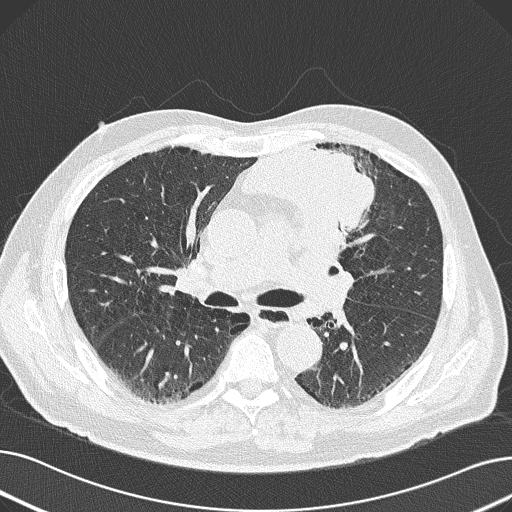
Axial slice from a low-dose chest CT screening exam. Baseline screening round. Lung window (W 1500 / L -600 HU). Lung (sharp) reconstruction kernel (B50f). 512 × 512 image matrix, field of view 370 × 370 mm. Male participant, aged 69 years at enrolment. Former smoker at enrolment.
Lesion marked by an expert reader, box from (x=236, y=132) to (x=385, y=249) px. Screening reader's record for this exam (one nodule recorded; not confirmed to be the boxed lesion): non-calcified nodule or mass ≥4 mm, left upper lobe, 6 × 10 mm, spiculated (stellate) margins, soft tissue attenuation. Official screen result: positive, change unspecified: nodule(s) >= 4 mm or enlarging nodule(s), mass(es), or other non-specific abnormalities suspicious for lung cancer. Lung cancer was diagnosed 20 days after this screen: non-small cell carcinoma, left upper lobe, poorly differentiated (G3), stage IB (AJCC 6th edition), 100 mm at pathology.